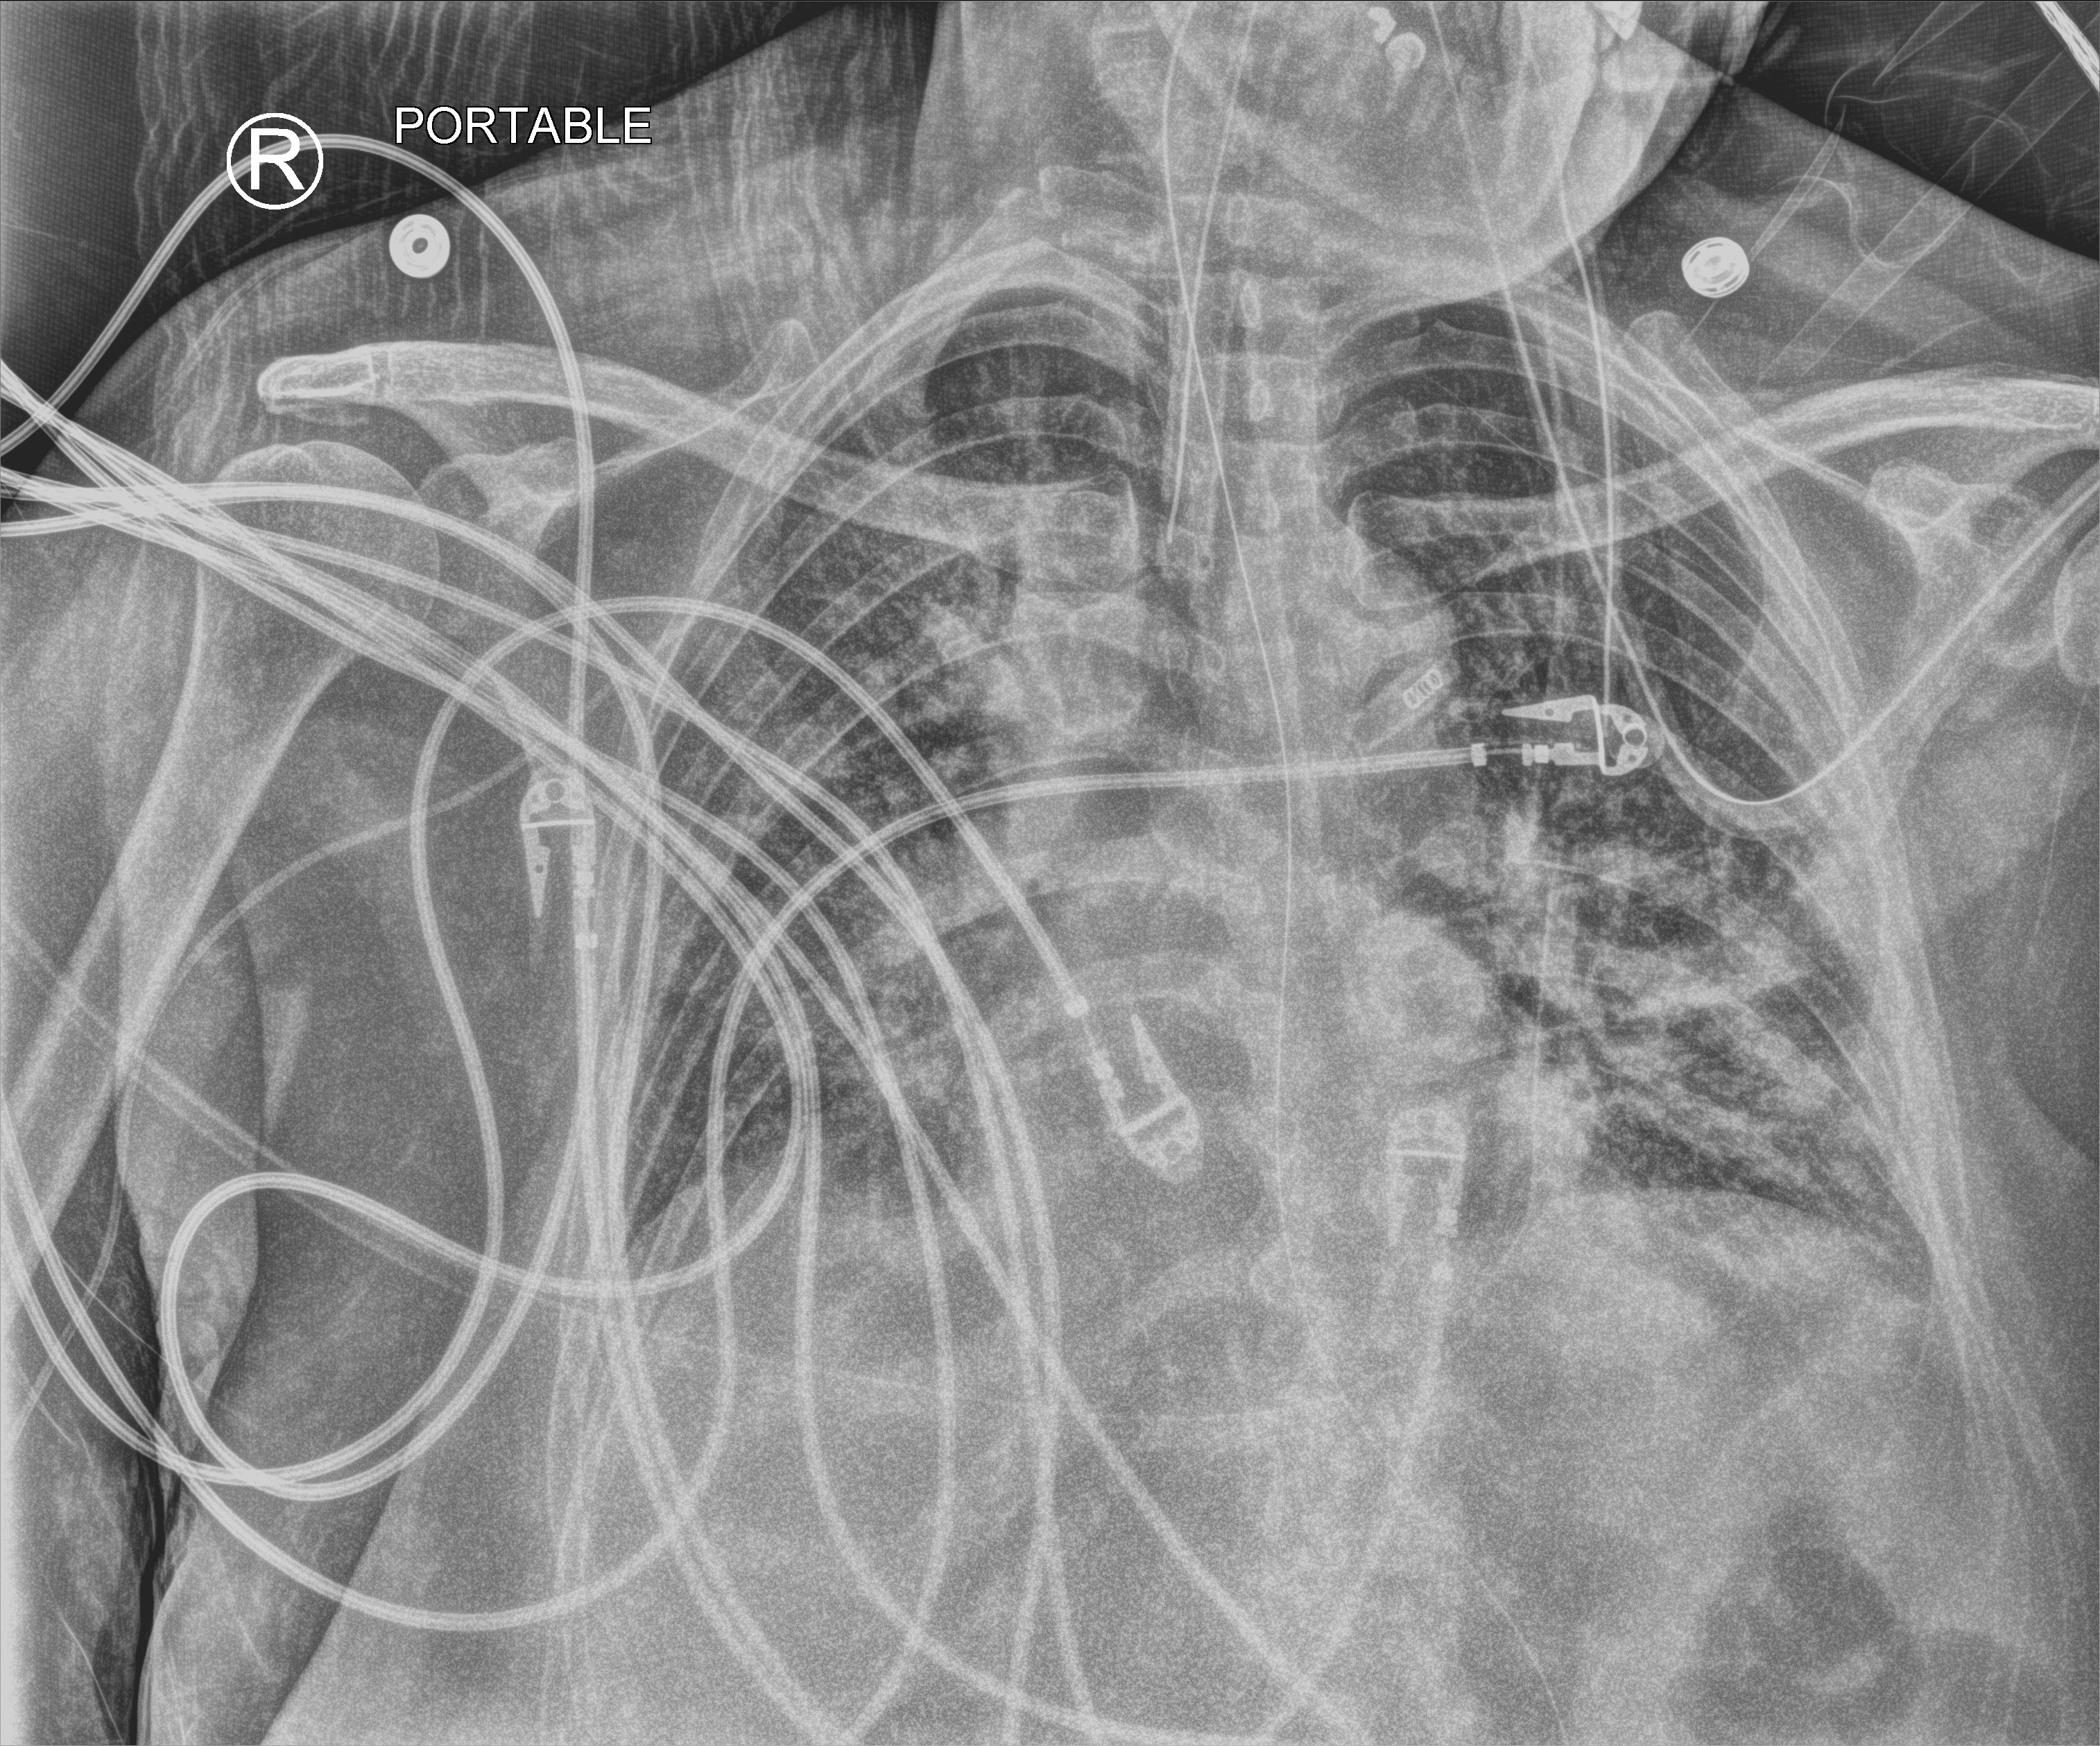
Portable chest radiograph. Female patient hospitalised with COVID-19, age 18–59 years.
Admission-level facts for this patient (not findings on this image; timing relative to this image not recorded): admitted to intensive care during this hospital stay: yes; mechanically ventilated during this hospital stay: yes.